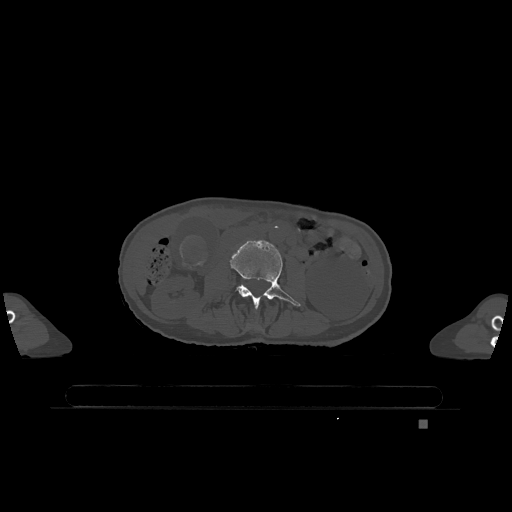
CT including the spine, one axial slice; bone window (W 1800 / L 400 HU); 0.5 mm slice thickness; 512 × 512 image matrix, field of view 500 × 500 mm. Patient: female, 74 years. From the clinical record (not read from this slice): primary cancer: lung; vertebrae with lytic lesions (as recorded): T1, T4, T5, T6, L4, L5.
Annotated regions visible in this slice (semi-automatic segmentation, software-assisted and operator-edited):
- L3 vertebra: bounding box (x1, y1, x2, y2) in pixels: (230, 240, 300, 309)